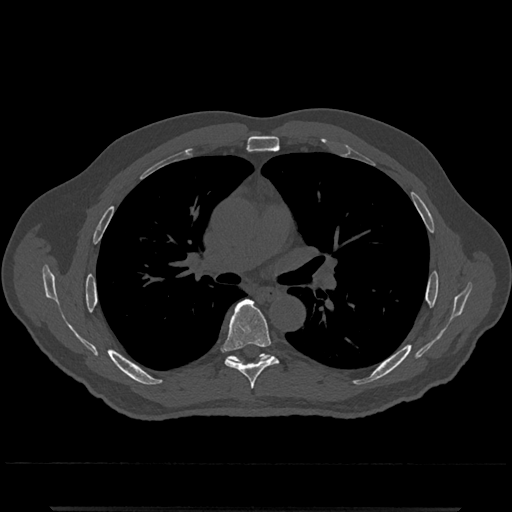
CT including the spine, one axial slice; position 765 of 797 along the scan axis; reconstruction kernel Br40s/3; bone window (W 1800 / L 400 HU); 512 × 512 image matrix, field of view 393 × 393 mm. Patient: male, 67 years. Case-level facts recorded for this patient, not image findings: primary cancer: prostate.
Outlined on this slice (semi-automatic segmentation, software-assisted and operator-edited):
- T6 vertebra: bounding box <221,300,278,389> (left, top, right, bottom; pixels)
- T7 vertebra: <227,354,271,363>